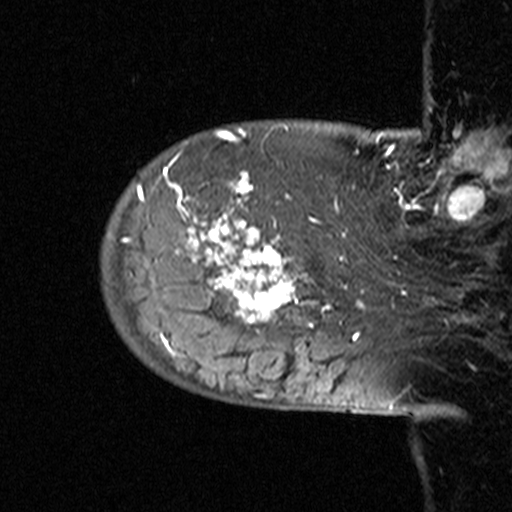
Breast MRI (dynamic contrast-enhanced), one sagittal slice. Position 8 of 44 along the scan axis. Dynamic contrast-enhanced study with each time point stored as its own series, time point 2 of 3 at this slice position (early post-contrast, ordered by acquisition time). 1.5 T. TE 4.5 ms, TR 11 ms. 3 mm slice thickness. 512 × 512 image matrix, field of view 200 × 200 mm. Patient: female, 53 years. Case-level facts recorded for this patient, not image findings: setting: breast cancer imaged before/during neoadjuvant chemotherapy; receptor status: HR-positive, HER2-negative.
Structures marked on this image (semi-automatic segmentation, software-assisted and operator-edited):
- analysis volume of interest (the breast-tissue region the enhancement analysis was run in; not a lesion): box from (x=99, y=140) to (x=311, y=353) px
- tumour enhancement mask (voxels above the 90 % enhancement threshold inside the analysis volume of interest): (x=122, y=140)–(x=306, y=340)